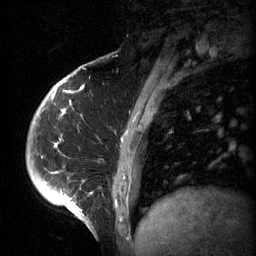
Breast MRI (dynamic contrast-enhanced), one sagittal slice; 3 images stored at this slice position (order not interpretable as contrast timing); 1.5 T; TE 4.2 ms, TR 11 ms; 256 × 256 image matrix, field of view 200 × 200 mm. Female patient, age 51 years.
Outlined on this slice (semi-automatically segmented with operator editing):
- analysis volume of interest (the breast-tissue region the enhancement analysis was run in; not a lesion): bounding box (x1, y1, x2, y2) in pixels: (48, 82, 161, 197)
- tumour enhancement mask (voxels above the 70 % enhancement threshold inside the analysis volume of interest): (48, 82, 149, 197)